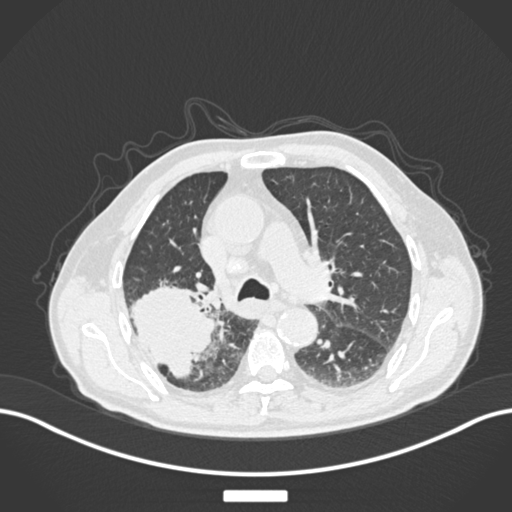
Chest CT, one axial slice. 120 kVp. Lung window (W 1500 / L -600 HU). 512 × 512 image matrix, field of view 400 × 400 mm. Patient: male, 72 years. Case-level facts recorded for this patient, not image findings: clinical TNM (as recorded): T3 N2 M0.
Outlined on this slice (rectangle marked by the reading radiologist):
- lung tumour (recorded histology: adenocarcinoma): bounding box <127,280,219,381> (left, top, right, bottom; pixels)